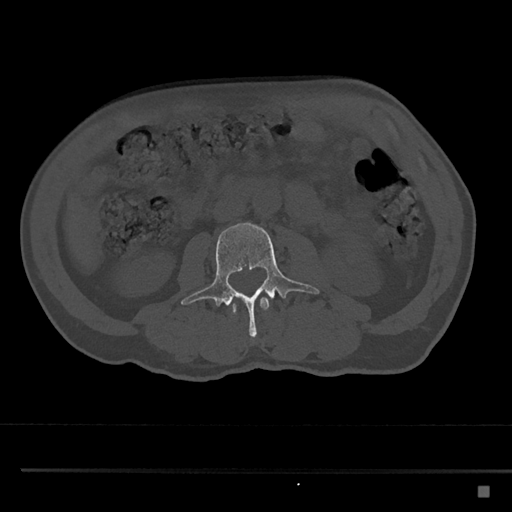
CT including the spine, one axial slice; slice 704 of 797 in the series (ordered by position); 120 kVp; bone window (W 1800 / L 400 HU); 0.5 mm slice thickness; 512 × 512 image matrix, field of view 391 × 391 mm. Male patient, age 59 years. From the clinical record (not read from this slice): primary cancer: prostate.
Structures marked on this image (semi-automatically segmented with operator editing):
- L2 vertebra: bounding box <228,297,269,315> (left, top, right, bottom; pixels)
- L3 vertebra: <181,222,320,339>